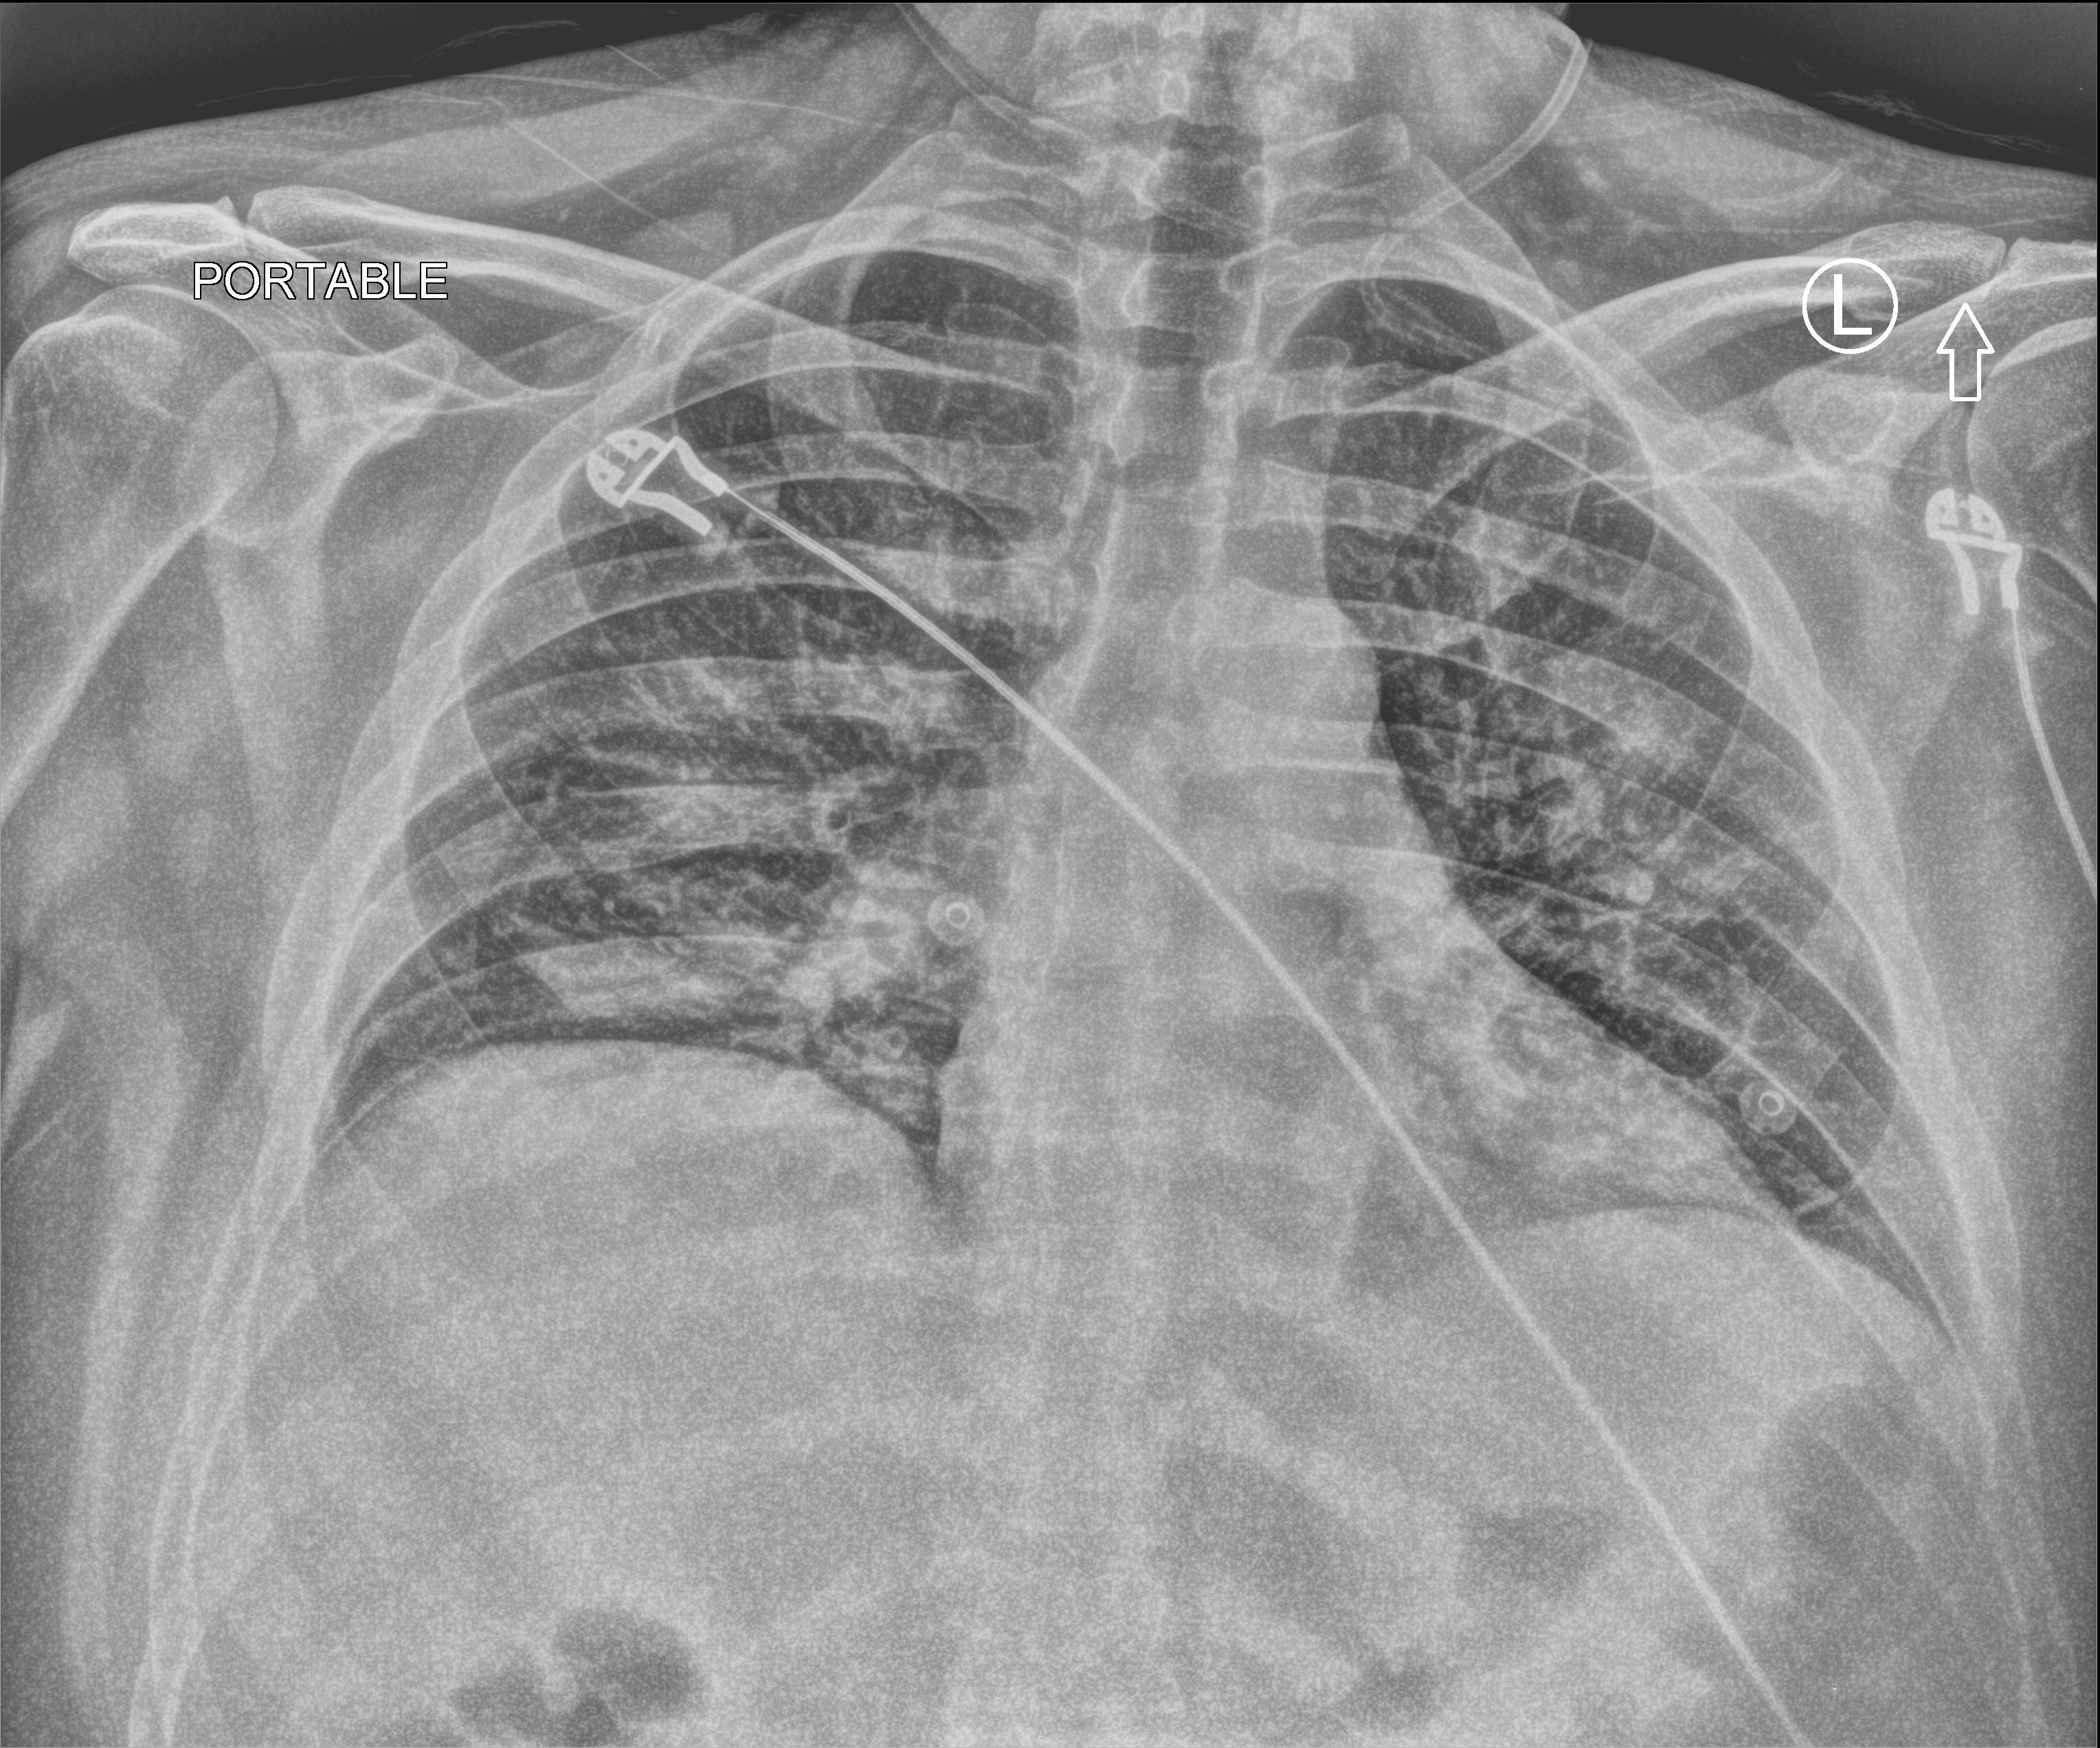
Portable chest radiograph, anteroposterior (AP) projection. Male patient hospitalised with COVID-19, age 18–59 years.
Admission-level facts for this patient (not findings on this image; timing relative to this image not recorded): admitted to intensive care during this hospital stay: no; other chronic lung disease (admission record): no; hypertension (admission record): no.